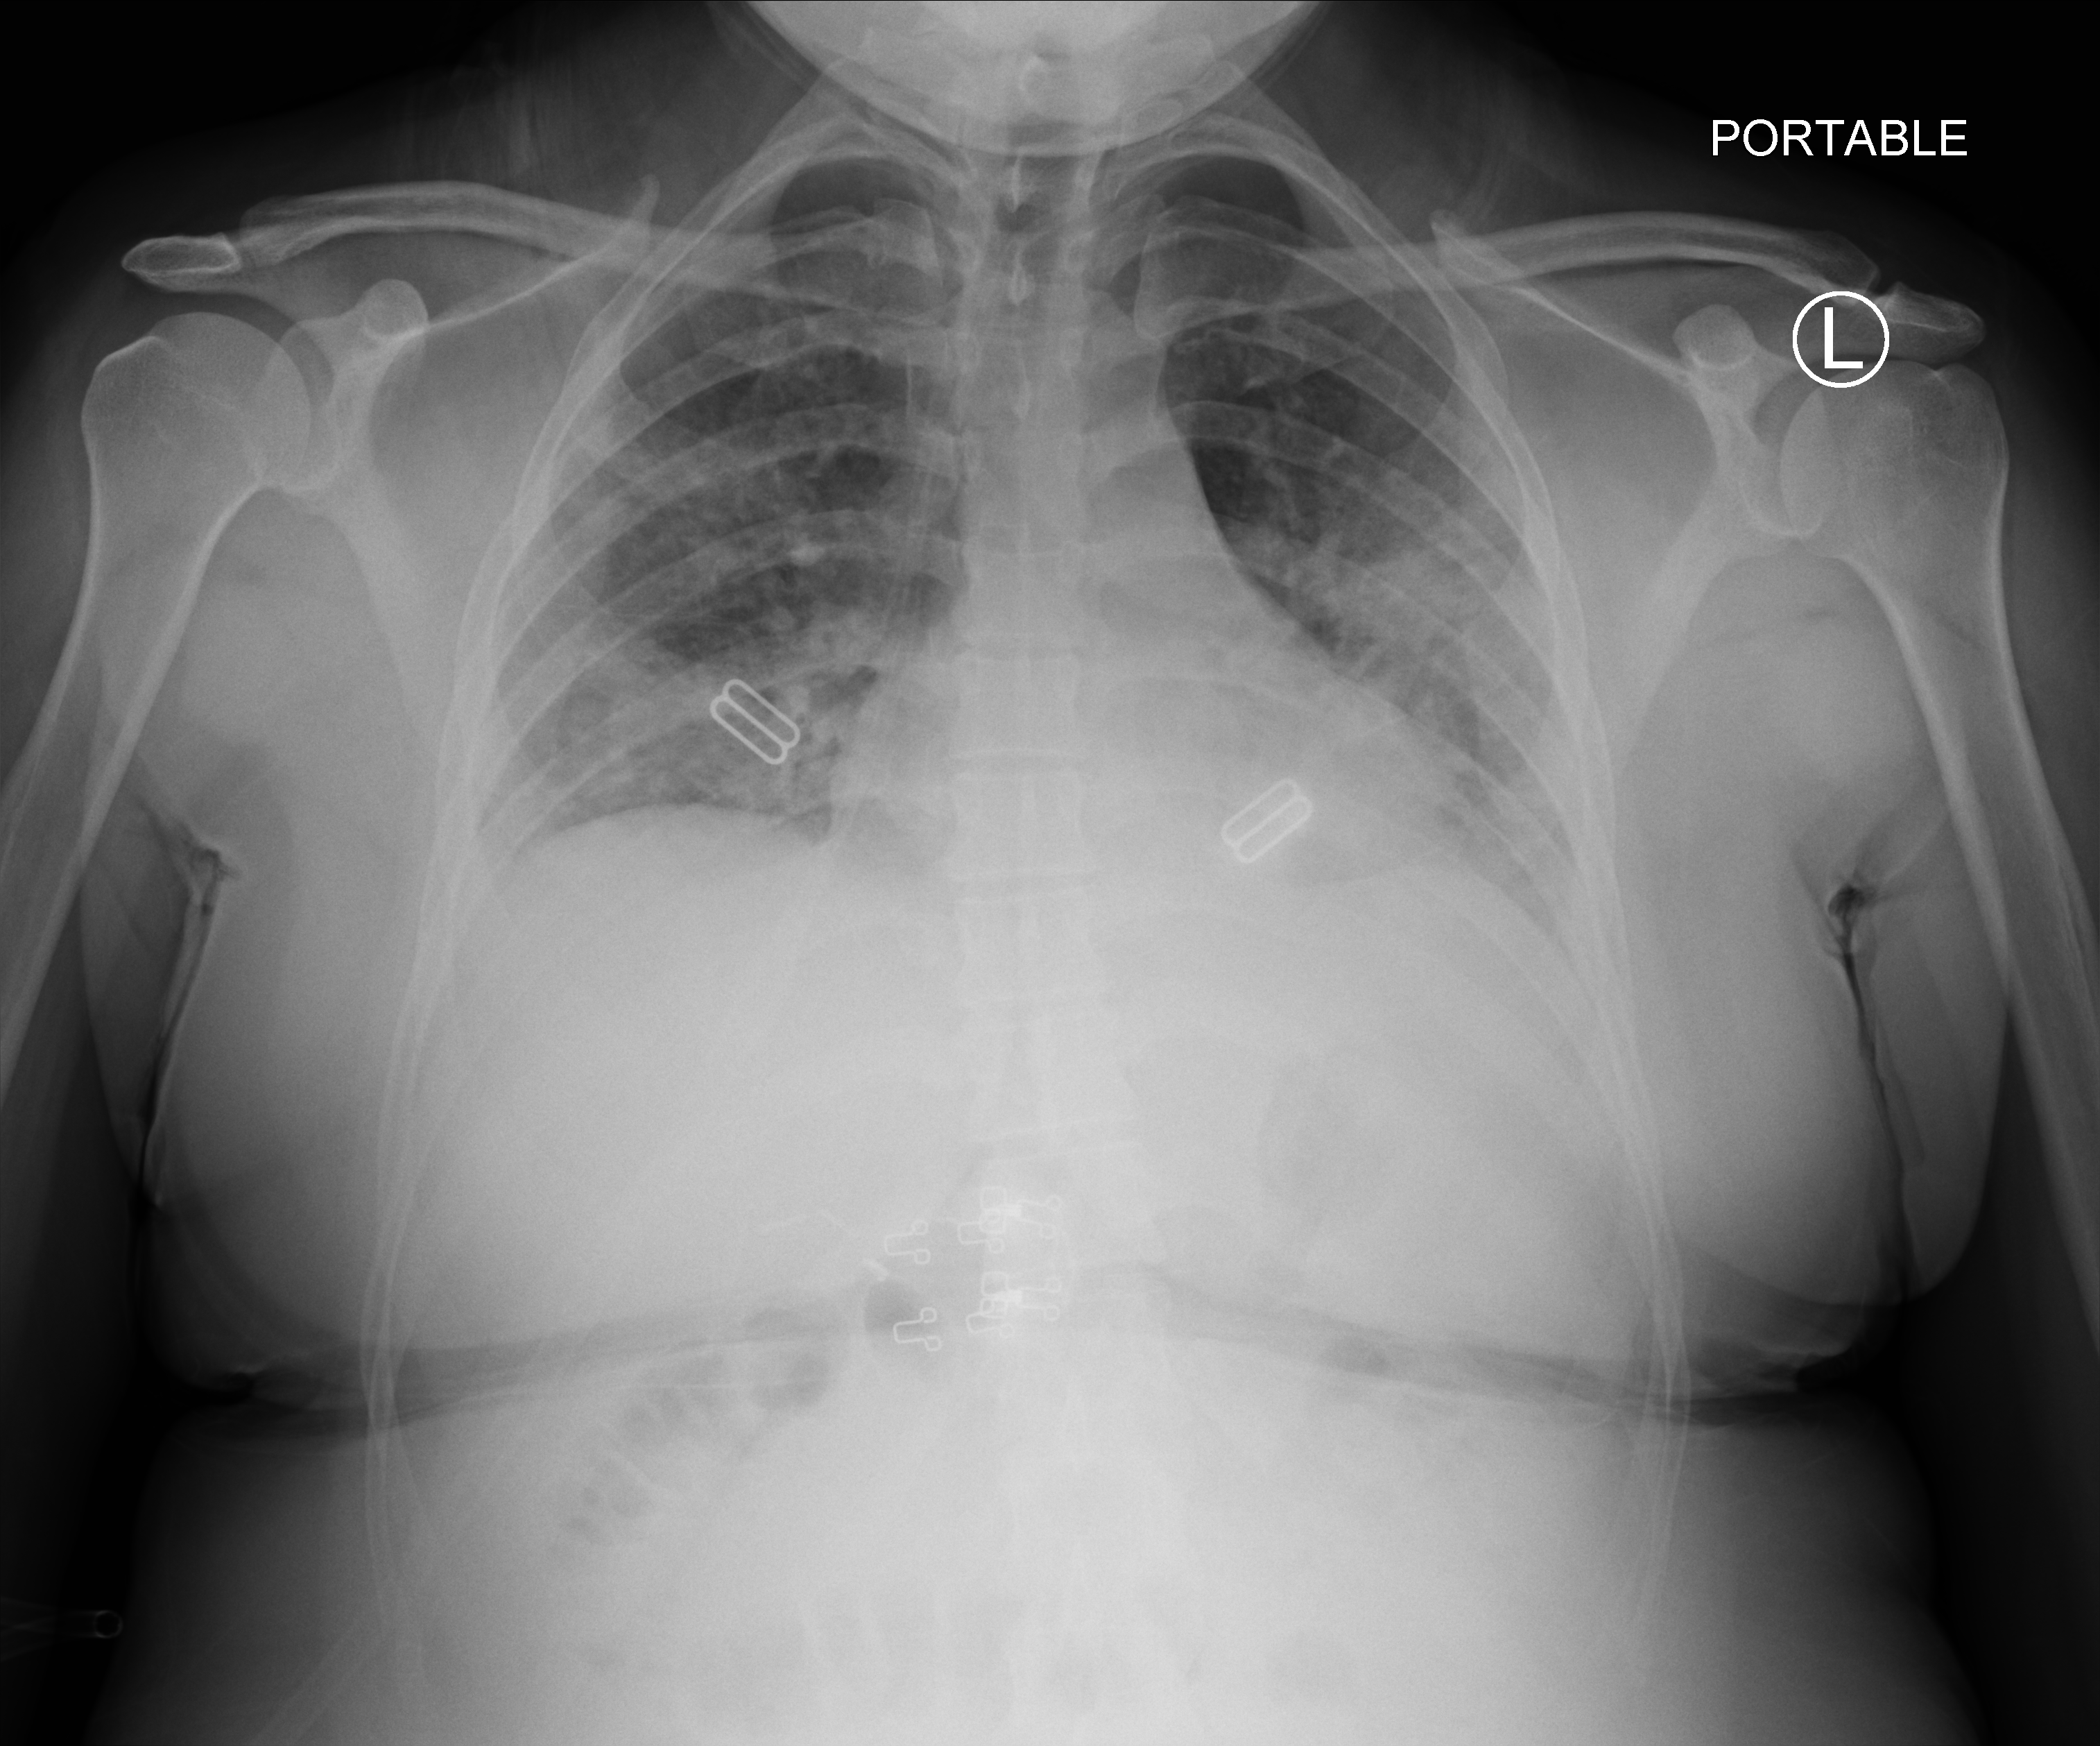
Bedside chest radiograph (computed radiography), anteroposterior (AP) projection. Female patient hospitalised with COVID-19, age 18–59 years.
Admission-level facts for this patient (not findings on this image; timing relative to this image not recorded): admitted to intensive care during this hospital stay: no; smoking status (admission record): never; mechanically ventilated during this hospital stay: no.